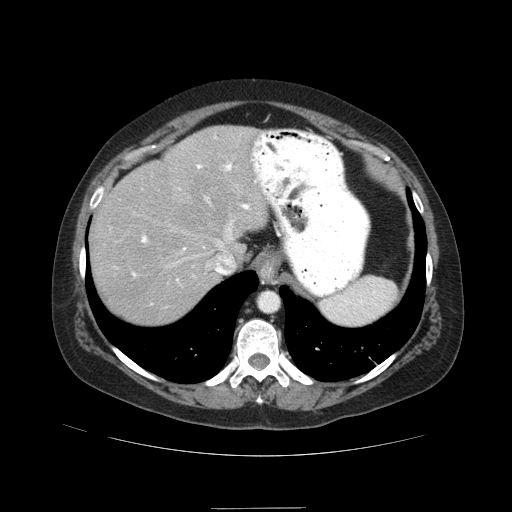
Contrast-enhanced abdominal CT (liver protocol), one axial slice; position 69 of 89 along the scan axis; 120 kVp; soft-tissue window (W 400 / L 40 HU); 2.5 mm slice thickness; 512 × 512 image matrix. From the clinical record (not read from this slice): diagnosis: hepatocellular carcinoma (patient treated with transarterial chemoembolisation; whether this scan precedes or follows treatment is not stated here); TNM stage (as recorded): Stage-IIIB.
Annotated regions visible in this slice (semi-automatically segmented with operator editing):
- abdominal aorta: bounding box [x1, y1, x2, y2] px = [259, 292, 278, 311]
- liver parenchyma outside the tumour (the mass and vessels are separate outlines, so this box may not span the whole liver): [90, 126, 268, 324]
- liver vessels: [133, 163, 257, 281]